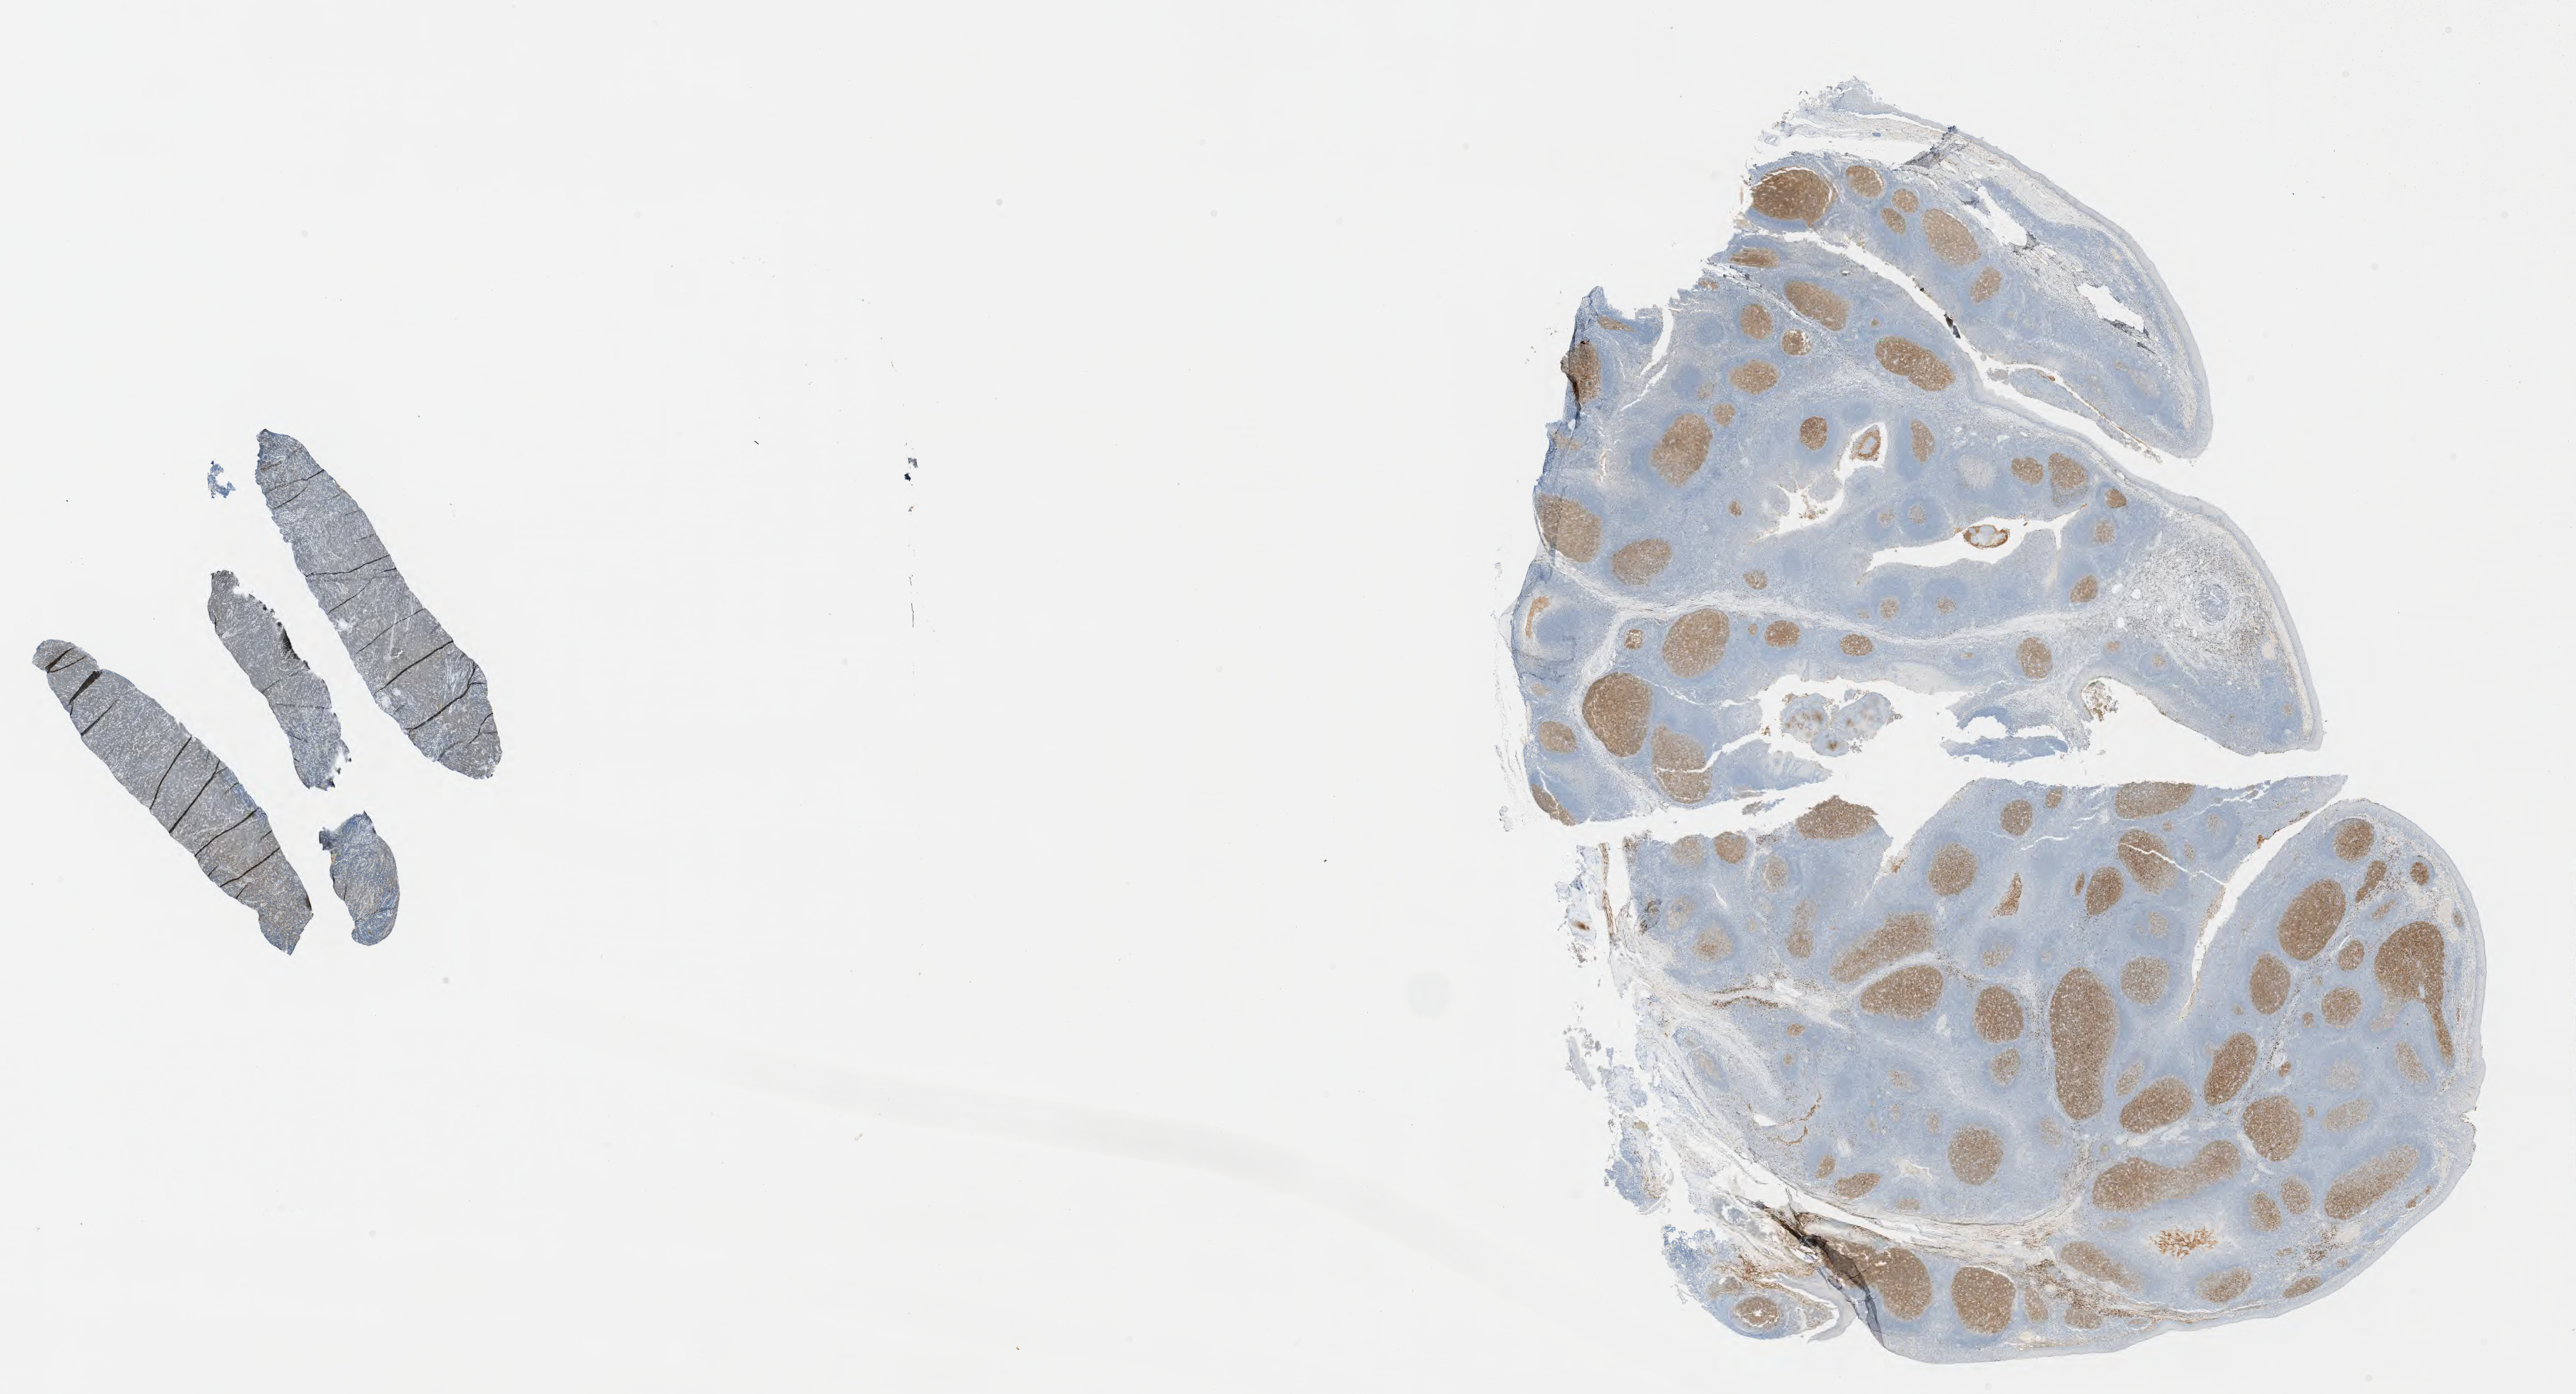
Whole-slide image, immunohistochemical stain for CD10, a low-resolution overview of the entire scanned area, about 29.2 x 15.8 mm; specimen: tumor tissue. Patient: female, age 46 years.
* histologic diagnosis: Burkitt lymphoma, NOS